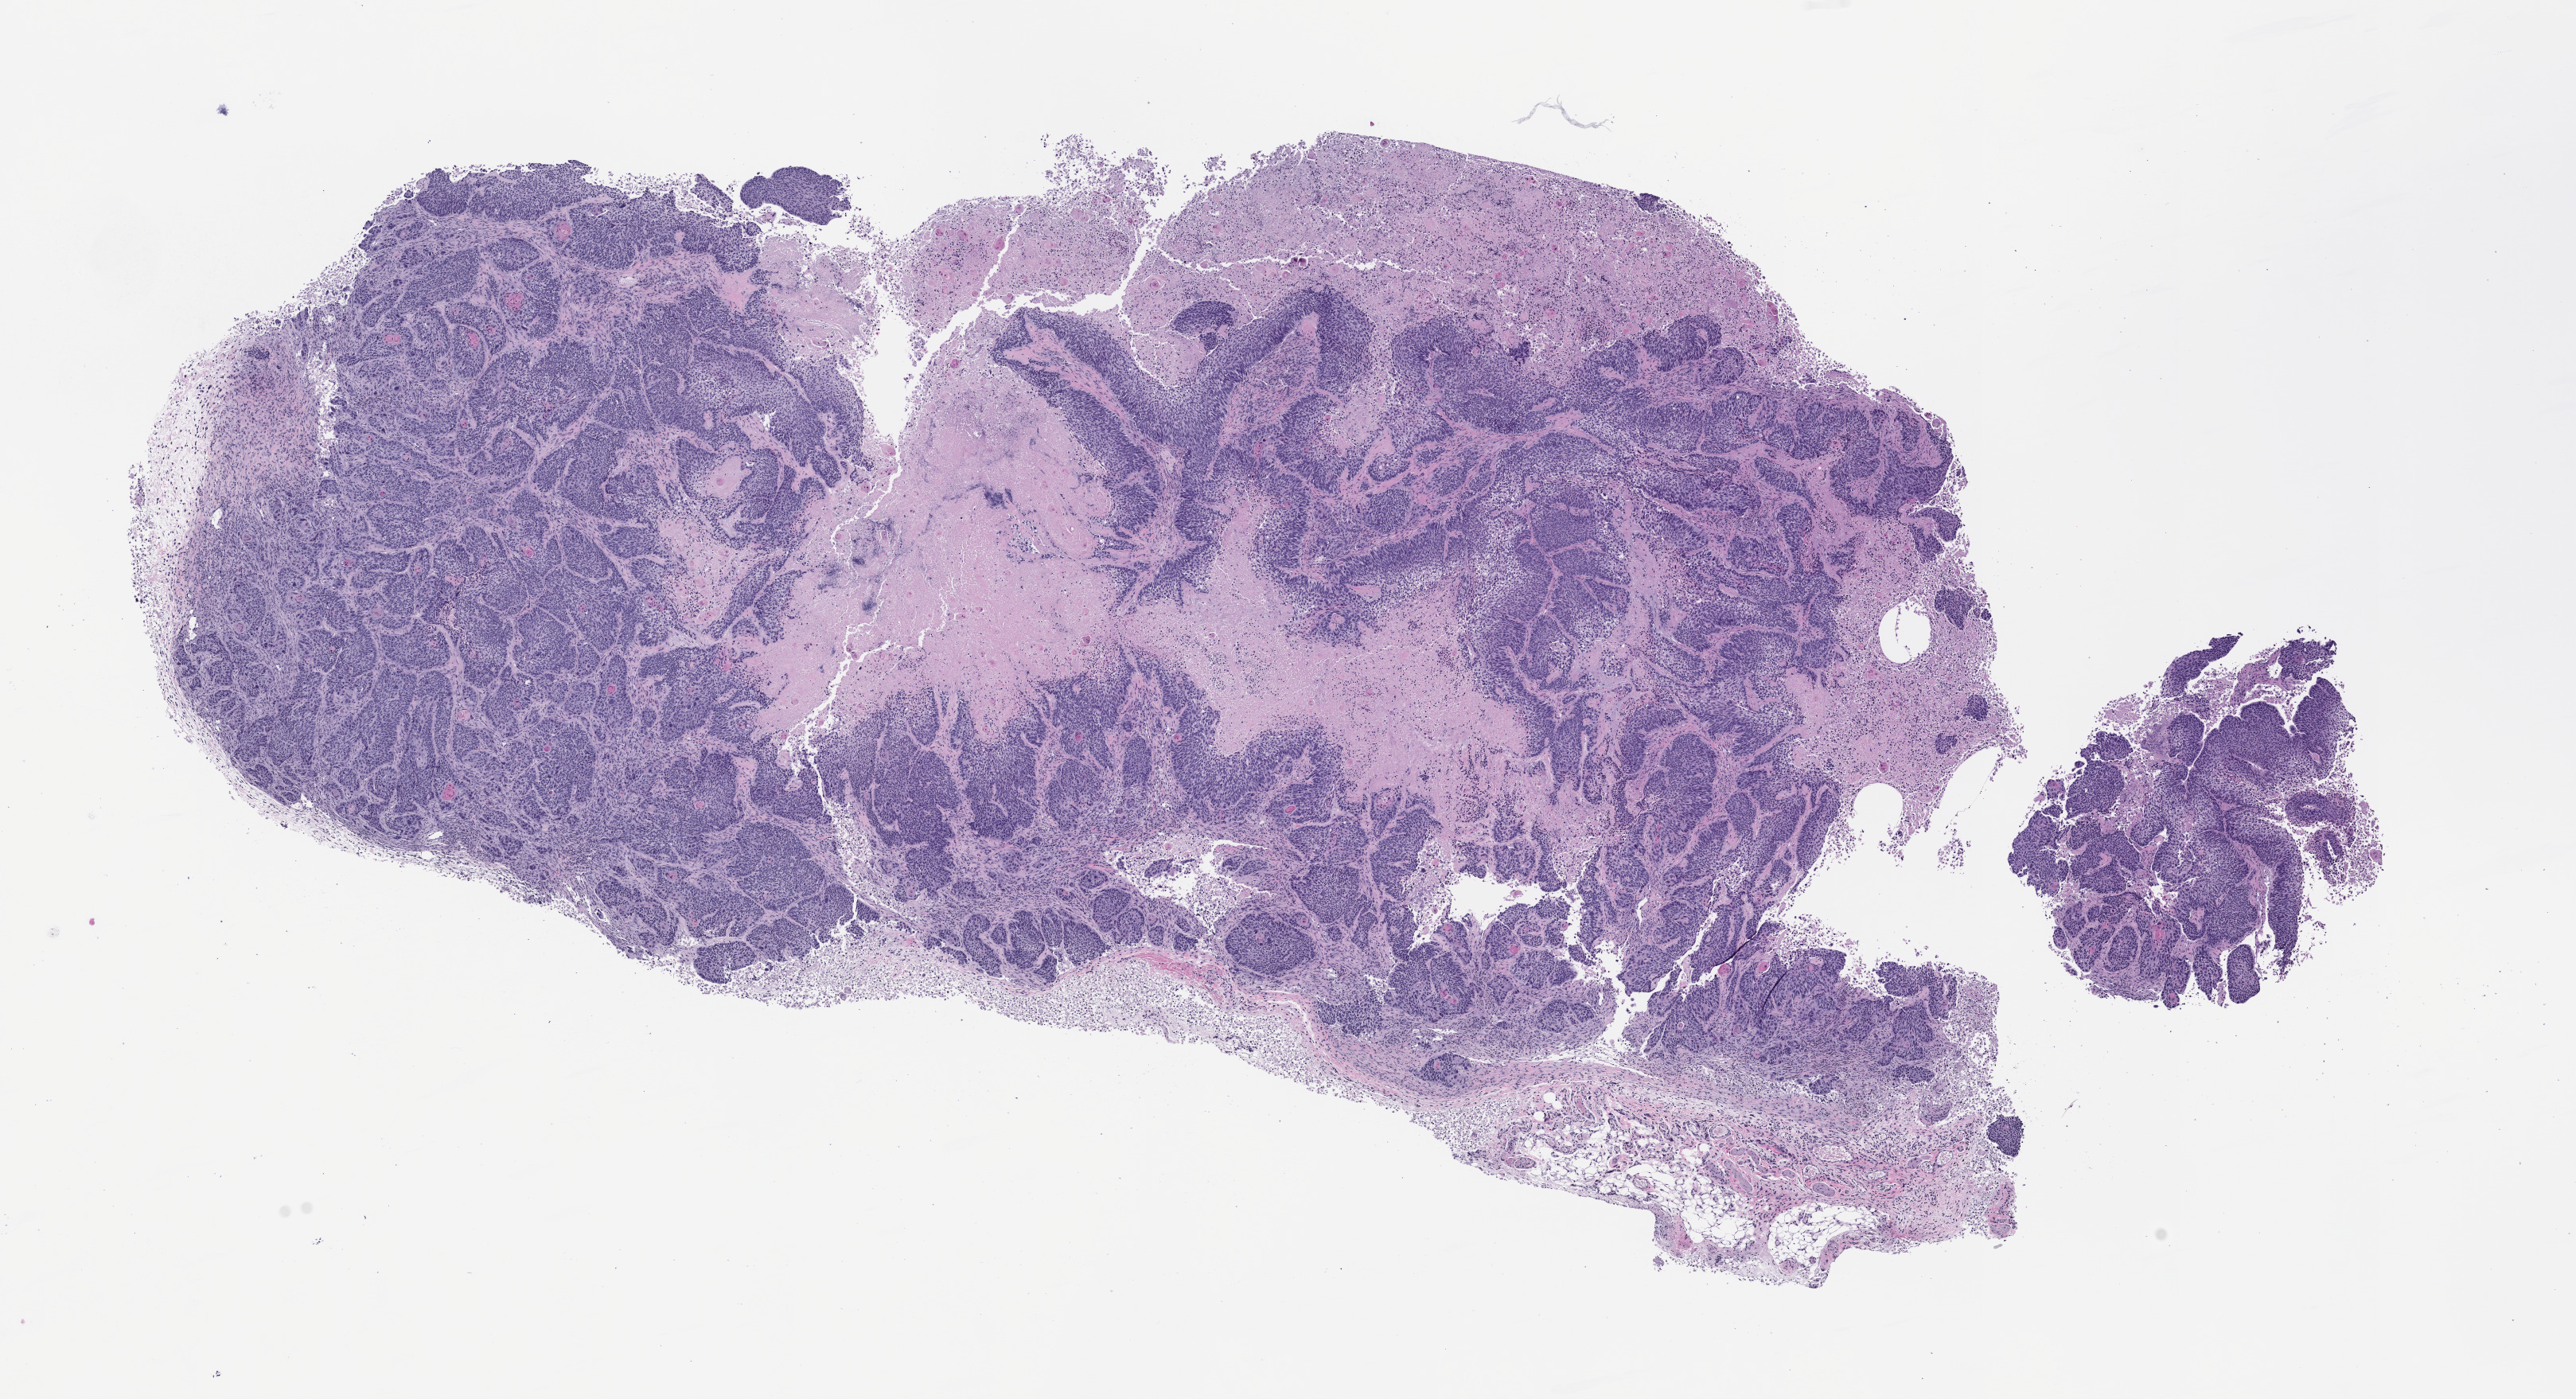
Haematoxylin and eosin whole-slide image of a patient-derived xenograft (PDX) tumor grown in a mouse, low-resolution overview of the scanned area, about 13.0 x 7.1 mm, formalin-fixed paraffin-embedded section, originating tumor site category: lung.
• originating patient diagnosis: Lung Squamous Cell Carcinoma